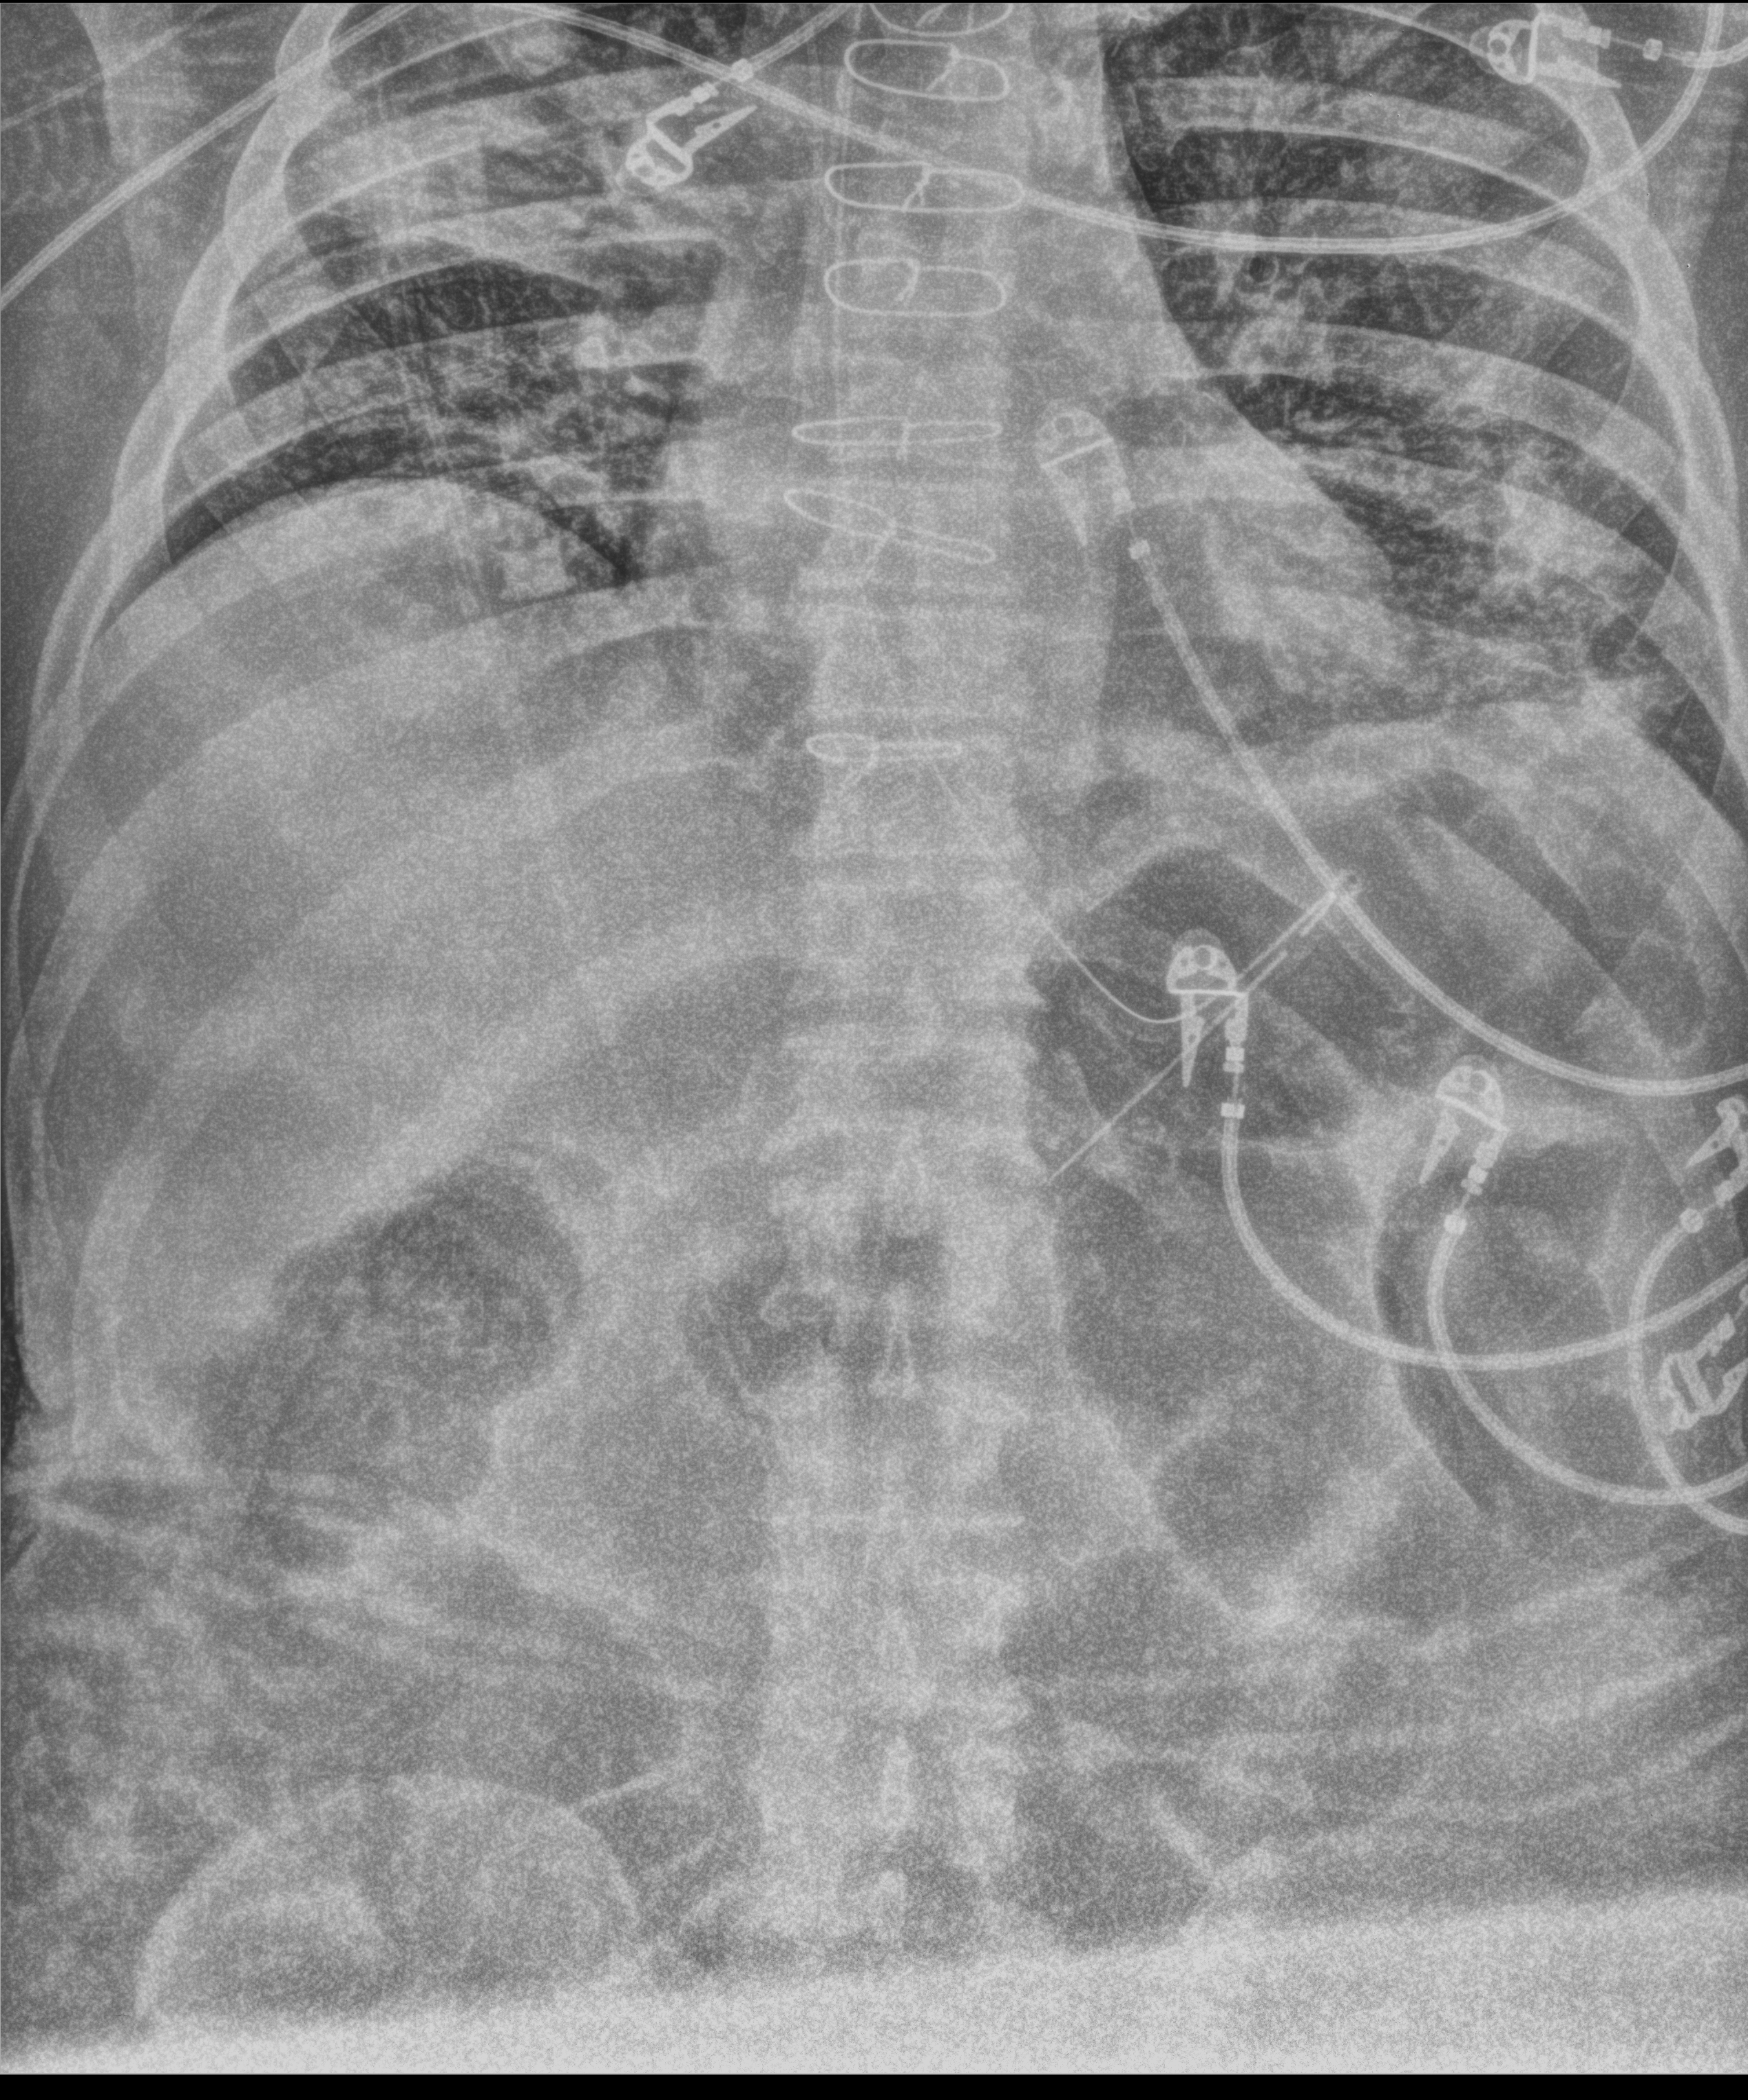
Bedside chest radiograph (computed radiography), anteroposterior (AP) projection. Patient hospitalised with COVID-19; male, aged 60–74 years.
Admission-level facts for this patient (not findings on this image; timing relative to this image not recorded): chronic kidney disease (admission record): no; mechanically ventilated during this hospital stay: yes; admitted to intensive care during this hospital stay: yes.